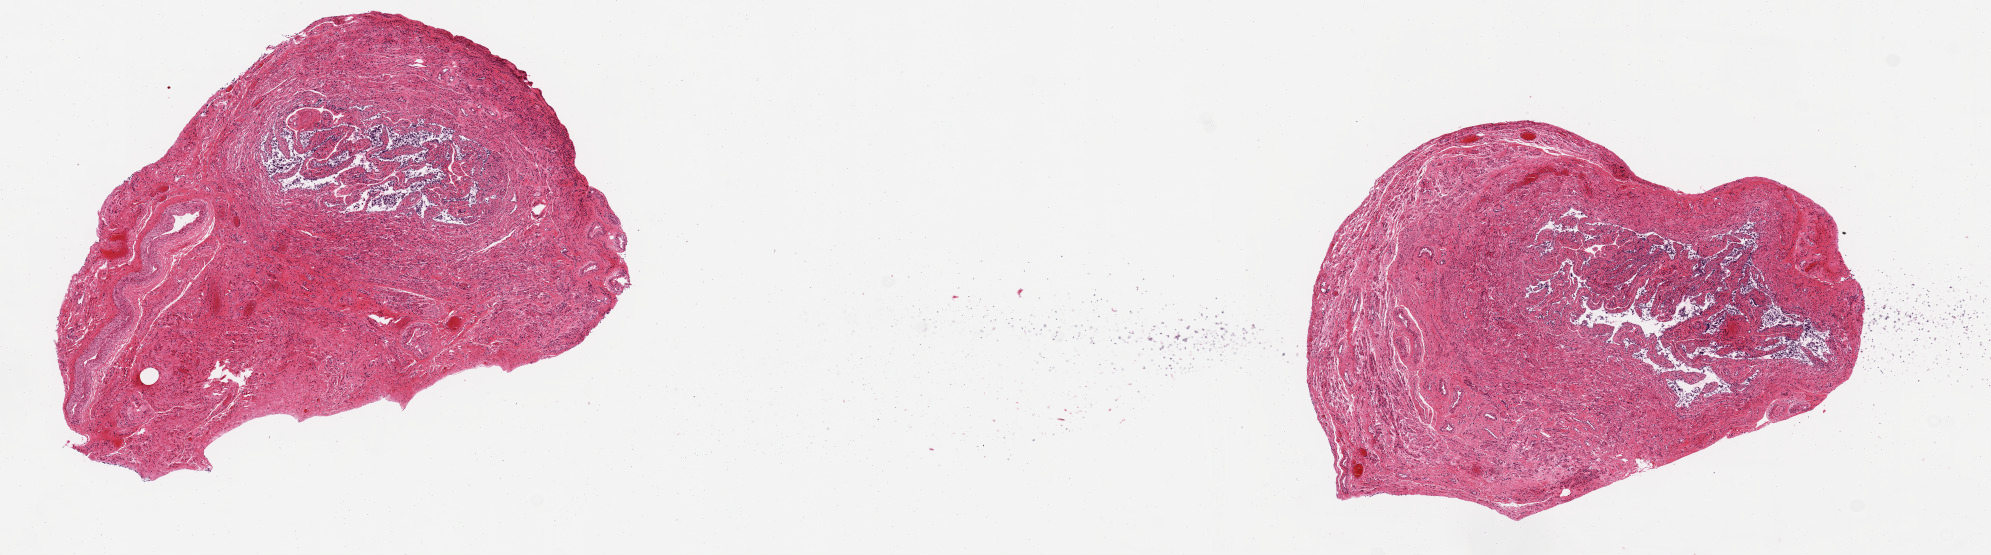
Whole-slide image, hematoxylin and eosin (H&E) stain, brightfield, a low-resolution overview of the entire scanned area, about 15.8 x 4.4 mm (acquisition: 20x scan). PAXgene-fixed, paraffin-embedded tissue. Sampled site (target tissue): fallopian tube. Donor tissue sample. Female donor.
Review note (as recorded): Epithelium, 1 wall. 2 pieces:.